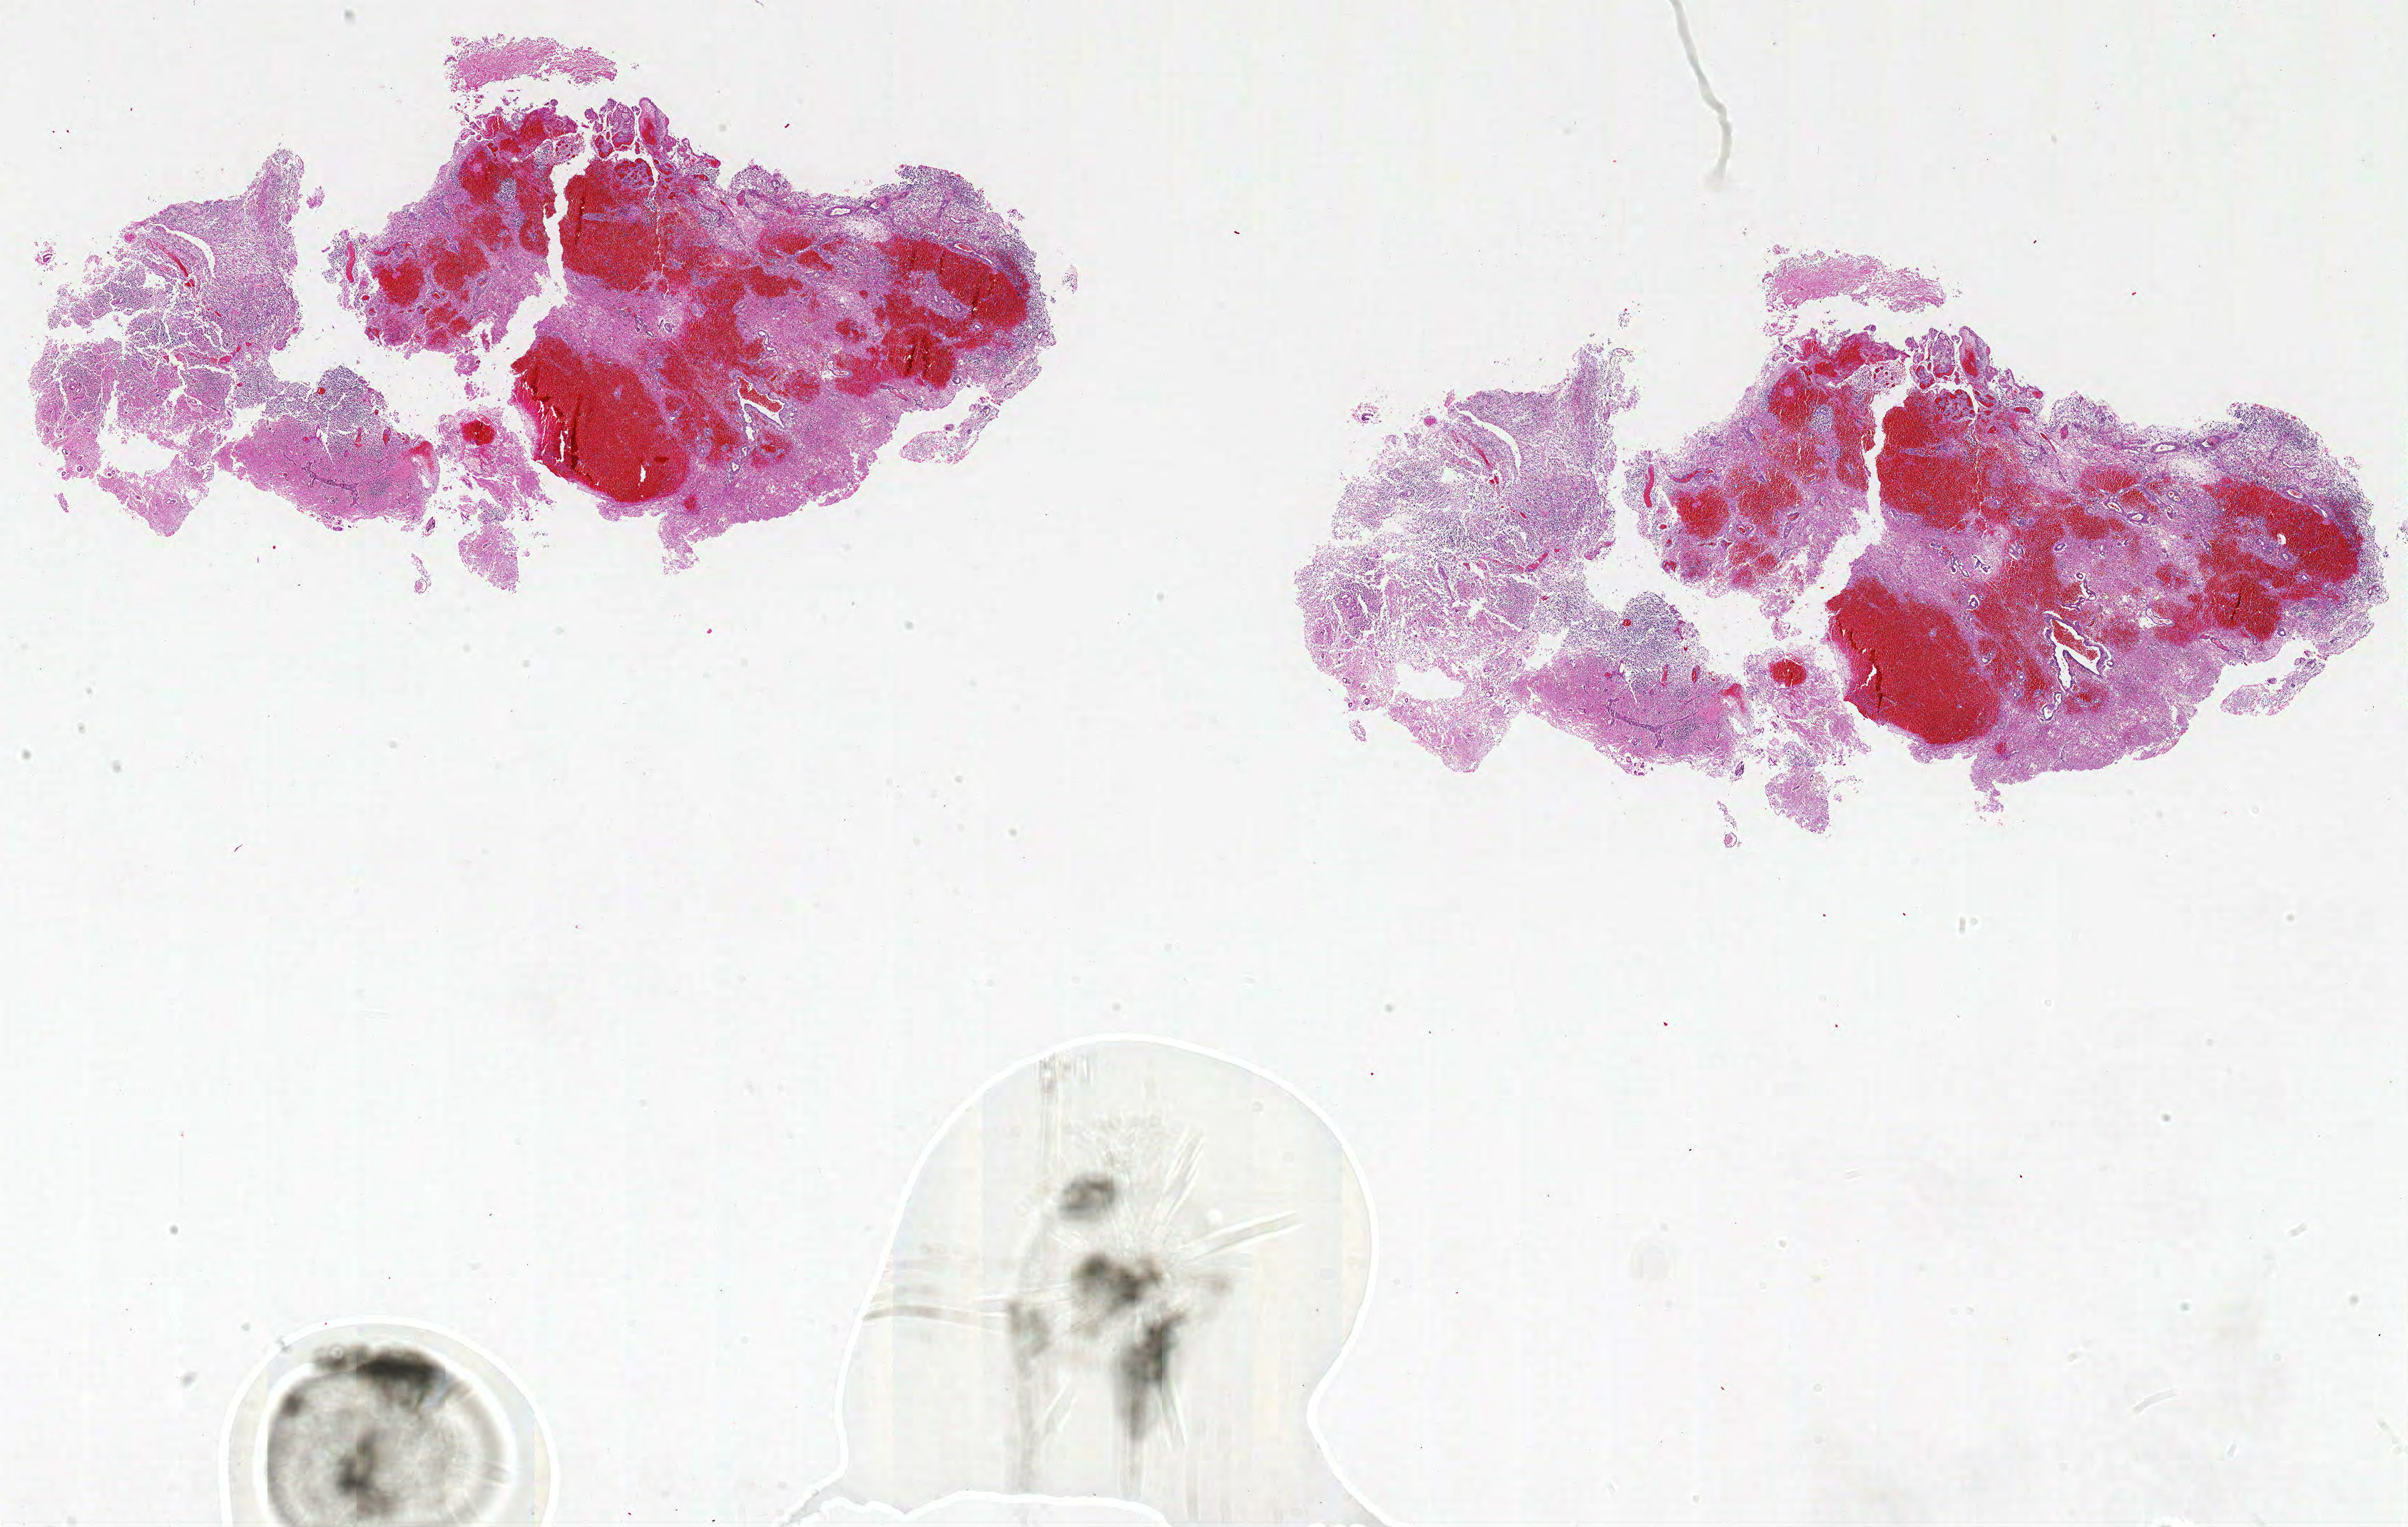
H&E-stained whole-slide image, a low-resolution overview of the entire scanned area, about 27.0 x 17.1 mm (slide scanned at 20x); formalin-fixed paraffin-embedded (FFPE) diagnostic section; brain, primary tumour sample. Female, age 47 years at initial diagnosis.
Pathologic diagnosis: Glioblastoma.